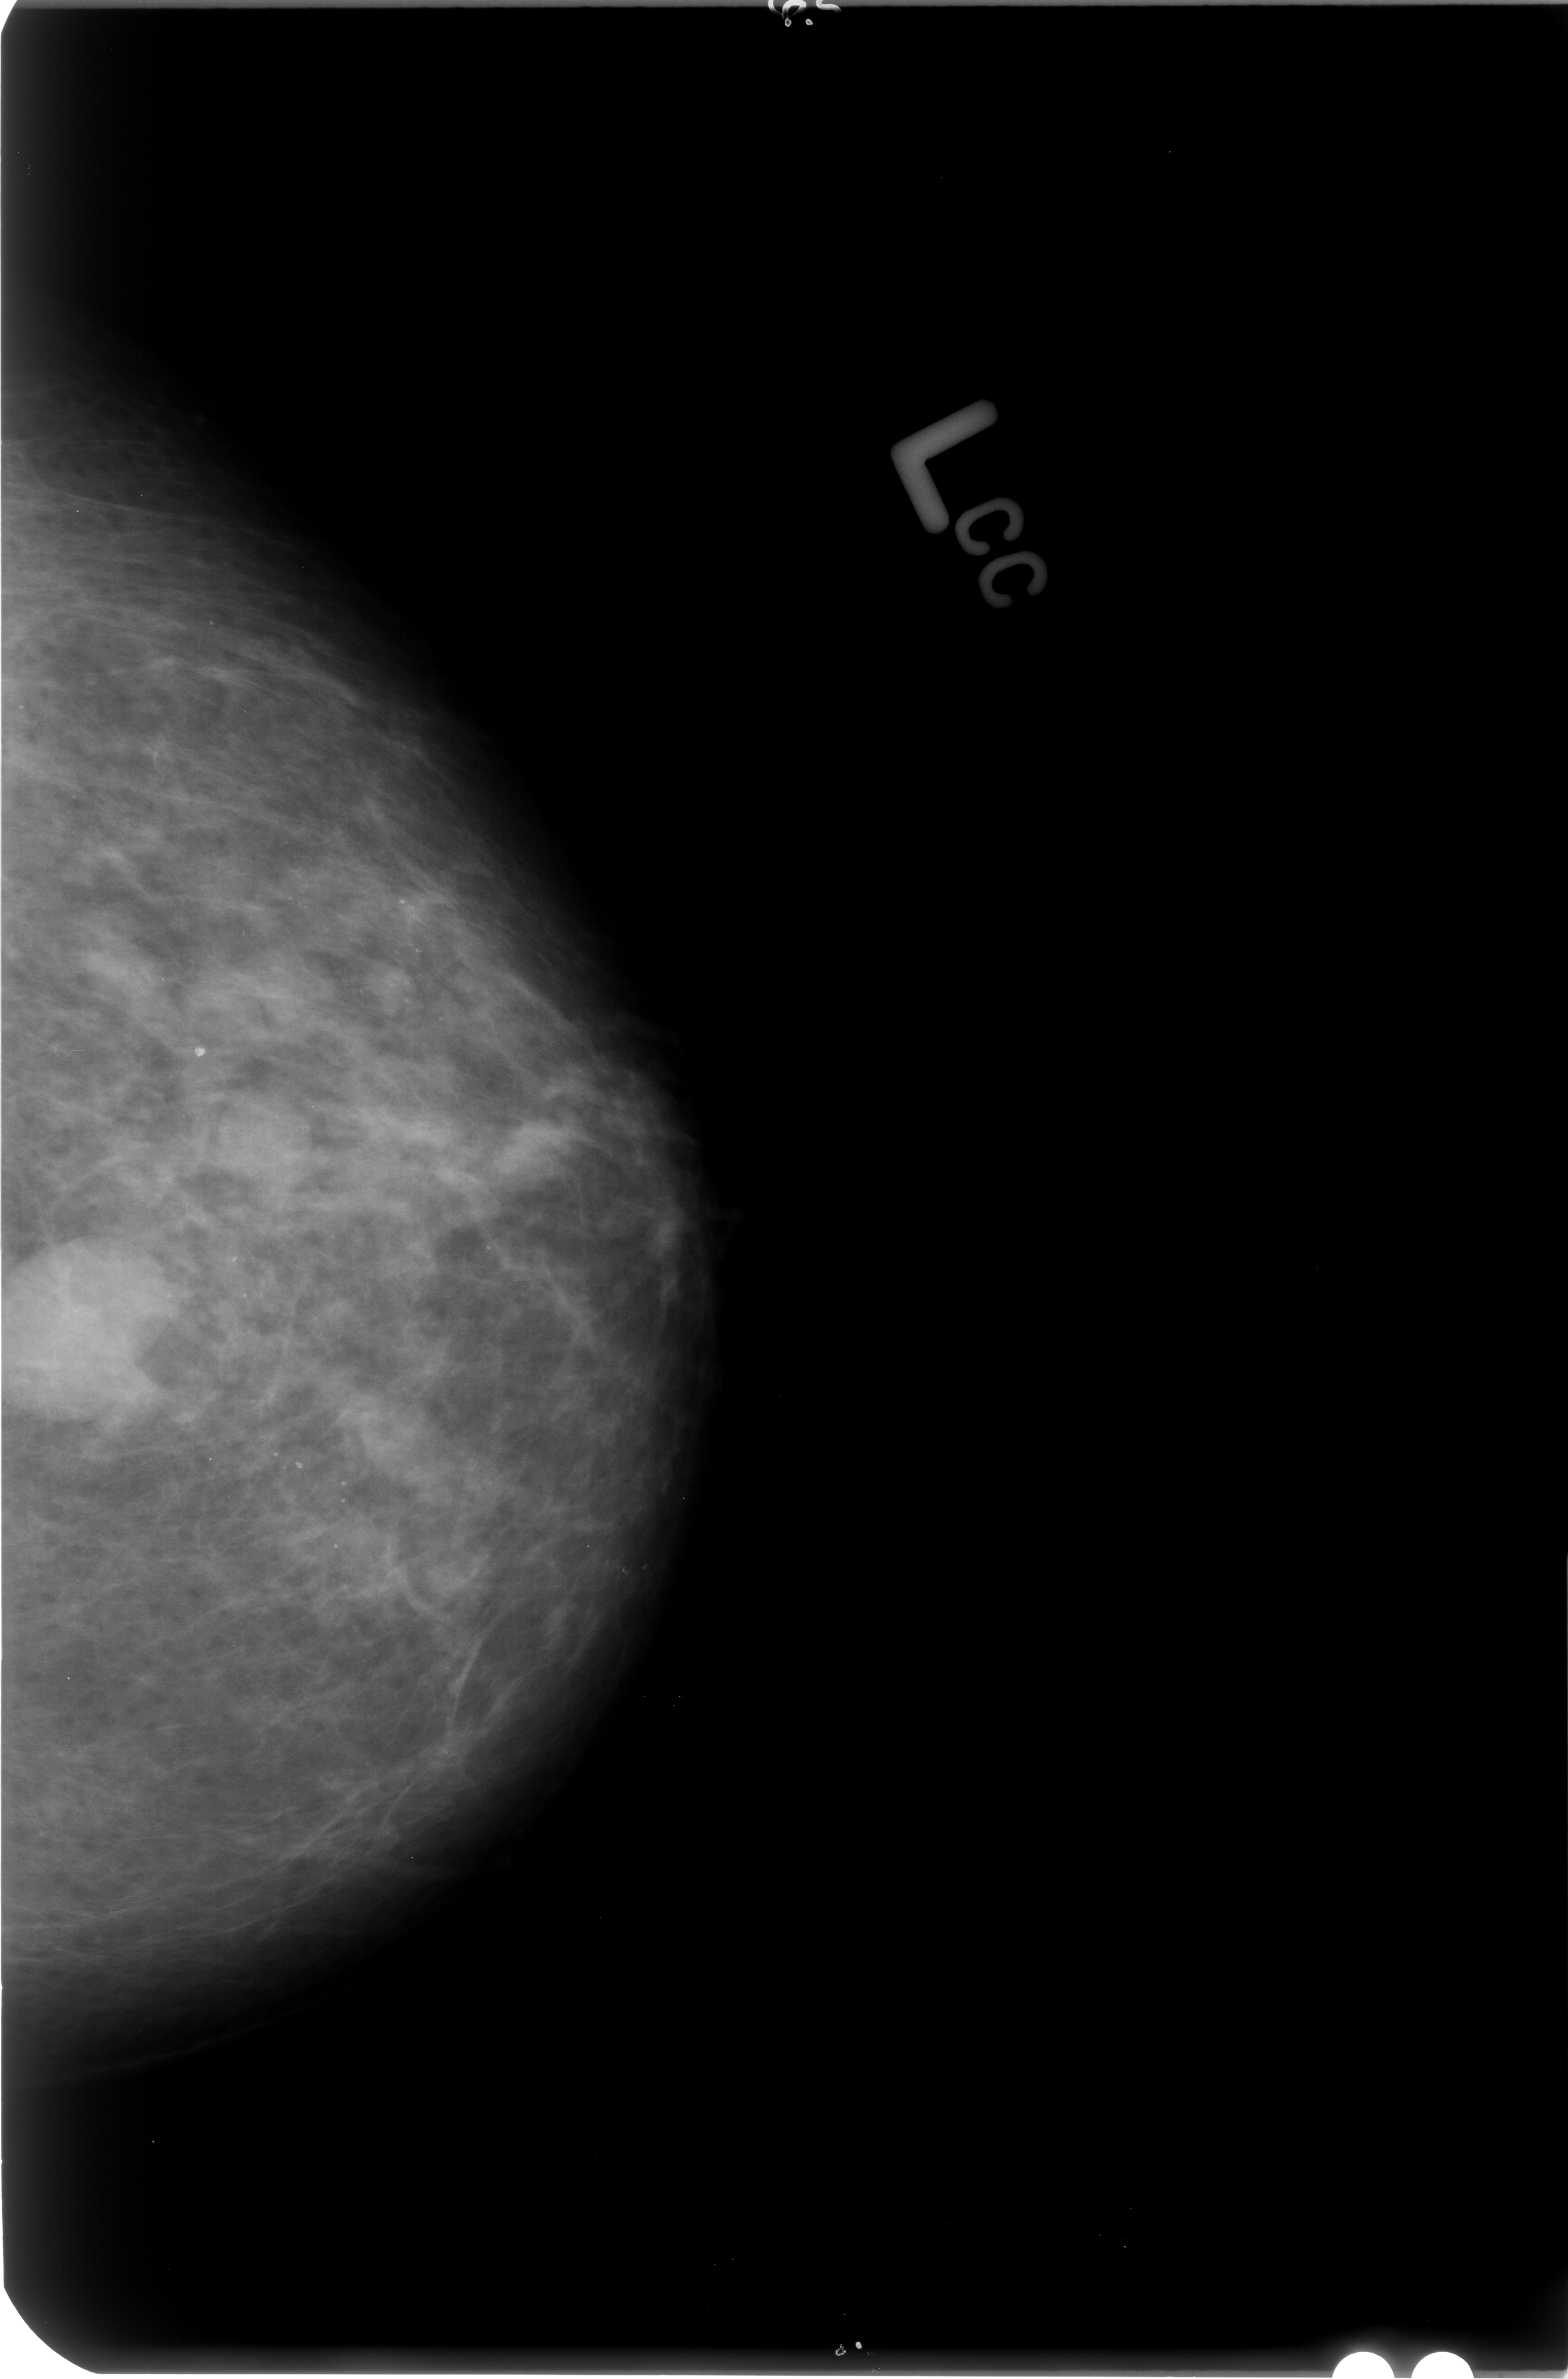
Digitized screen-film mammogram; left breast; CC view; breast composition: scattered fibroglandular densities (BI-RADS density category 2 of 4).
- Marked findings (only marked abnormalities are described; nothing is implied about the rest of the image): Finding 1 of 2: mass, shape round / oval, margins circumscribed / obscured; BI-RADS assessment category 4; pathology result (as recorded, not read from the image): benign.
- Finding 2 of 2: mass, shape round / oval, margins circumscribed / obscured; BI-RADS assessment category 4; pathology result (as recorded, not read from the image): benign.